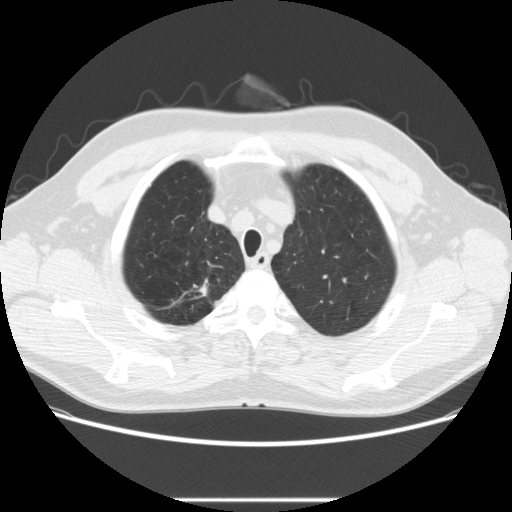
Chest CT (low-dose screening protocol), one axial image. First (baseline) screen. Lung window (W 1500 / L -600 HU). 2.5 mm slice thickness. Standard (soft-tissue) reconstruction kernel (STANDARD). Male, age 64 years at enrolment. Former smoker at enrolment.
Expert reader's lesion annotation, bounding box [x1, y1, x2, y2] px = [174, 279, 218, 308]. The screening reader recorded 2 non-calcified nodules or masses ≥4 mm on this exam (right upper lobe, right upper lobe); which of them this box marks is not recorded. Participant outcome: lung cancer diagnosed 753 days after this screen (after the third annual screen) — adenocarcinoma, NOS, right upper lobe, moderately differentiated (G2), stage IA (AJCC 6th edition), 14 mm at pathology.